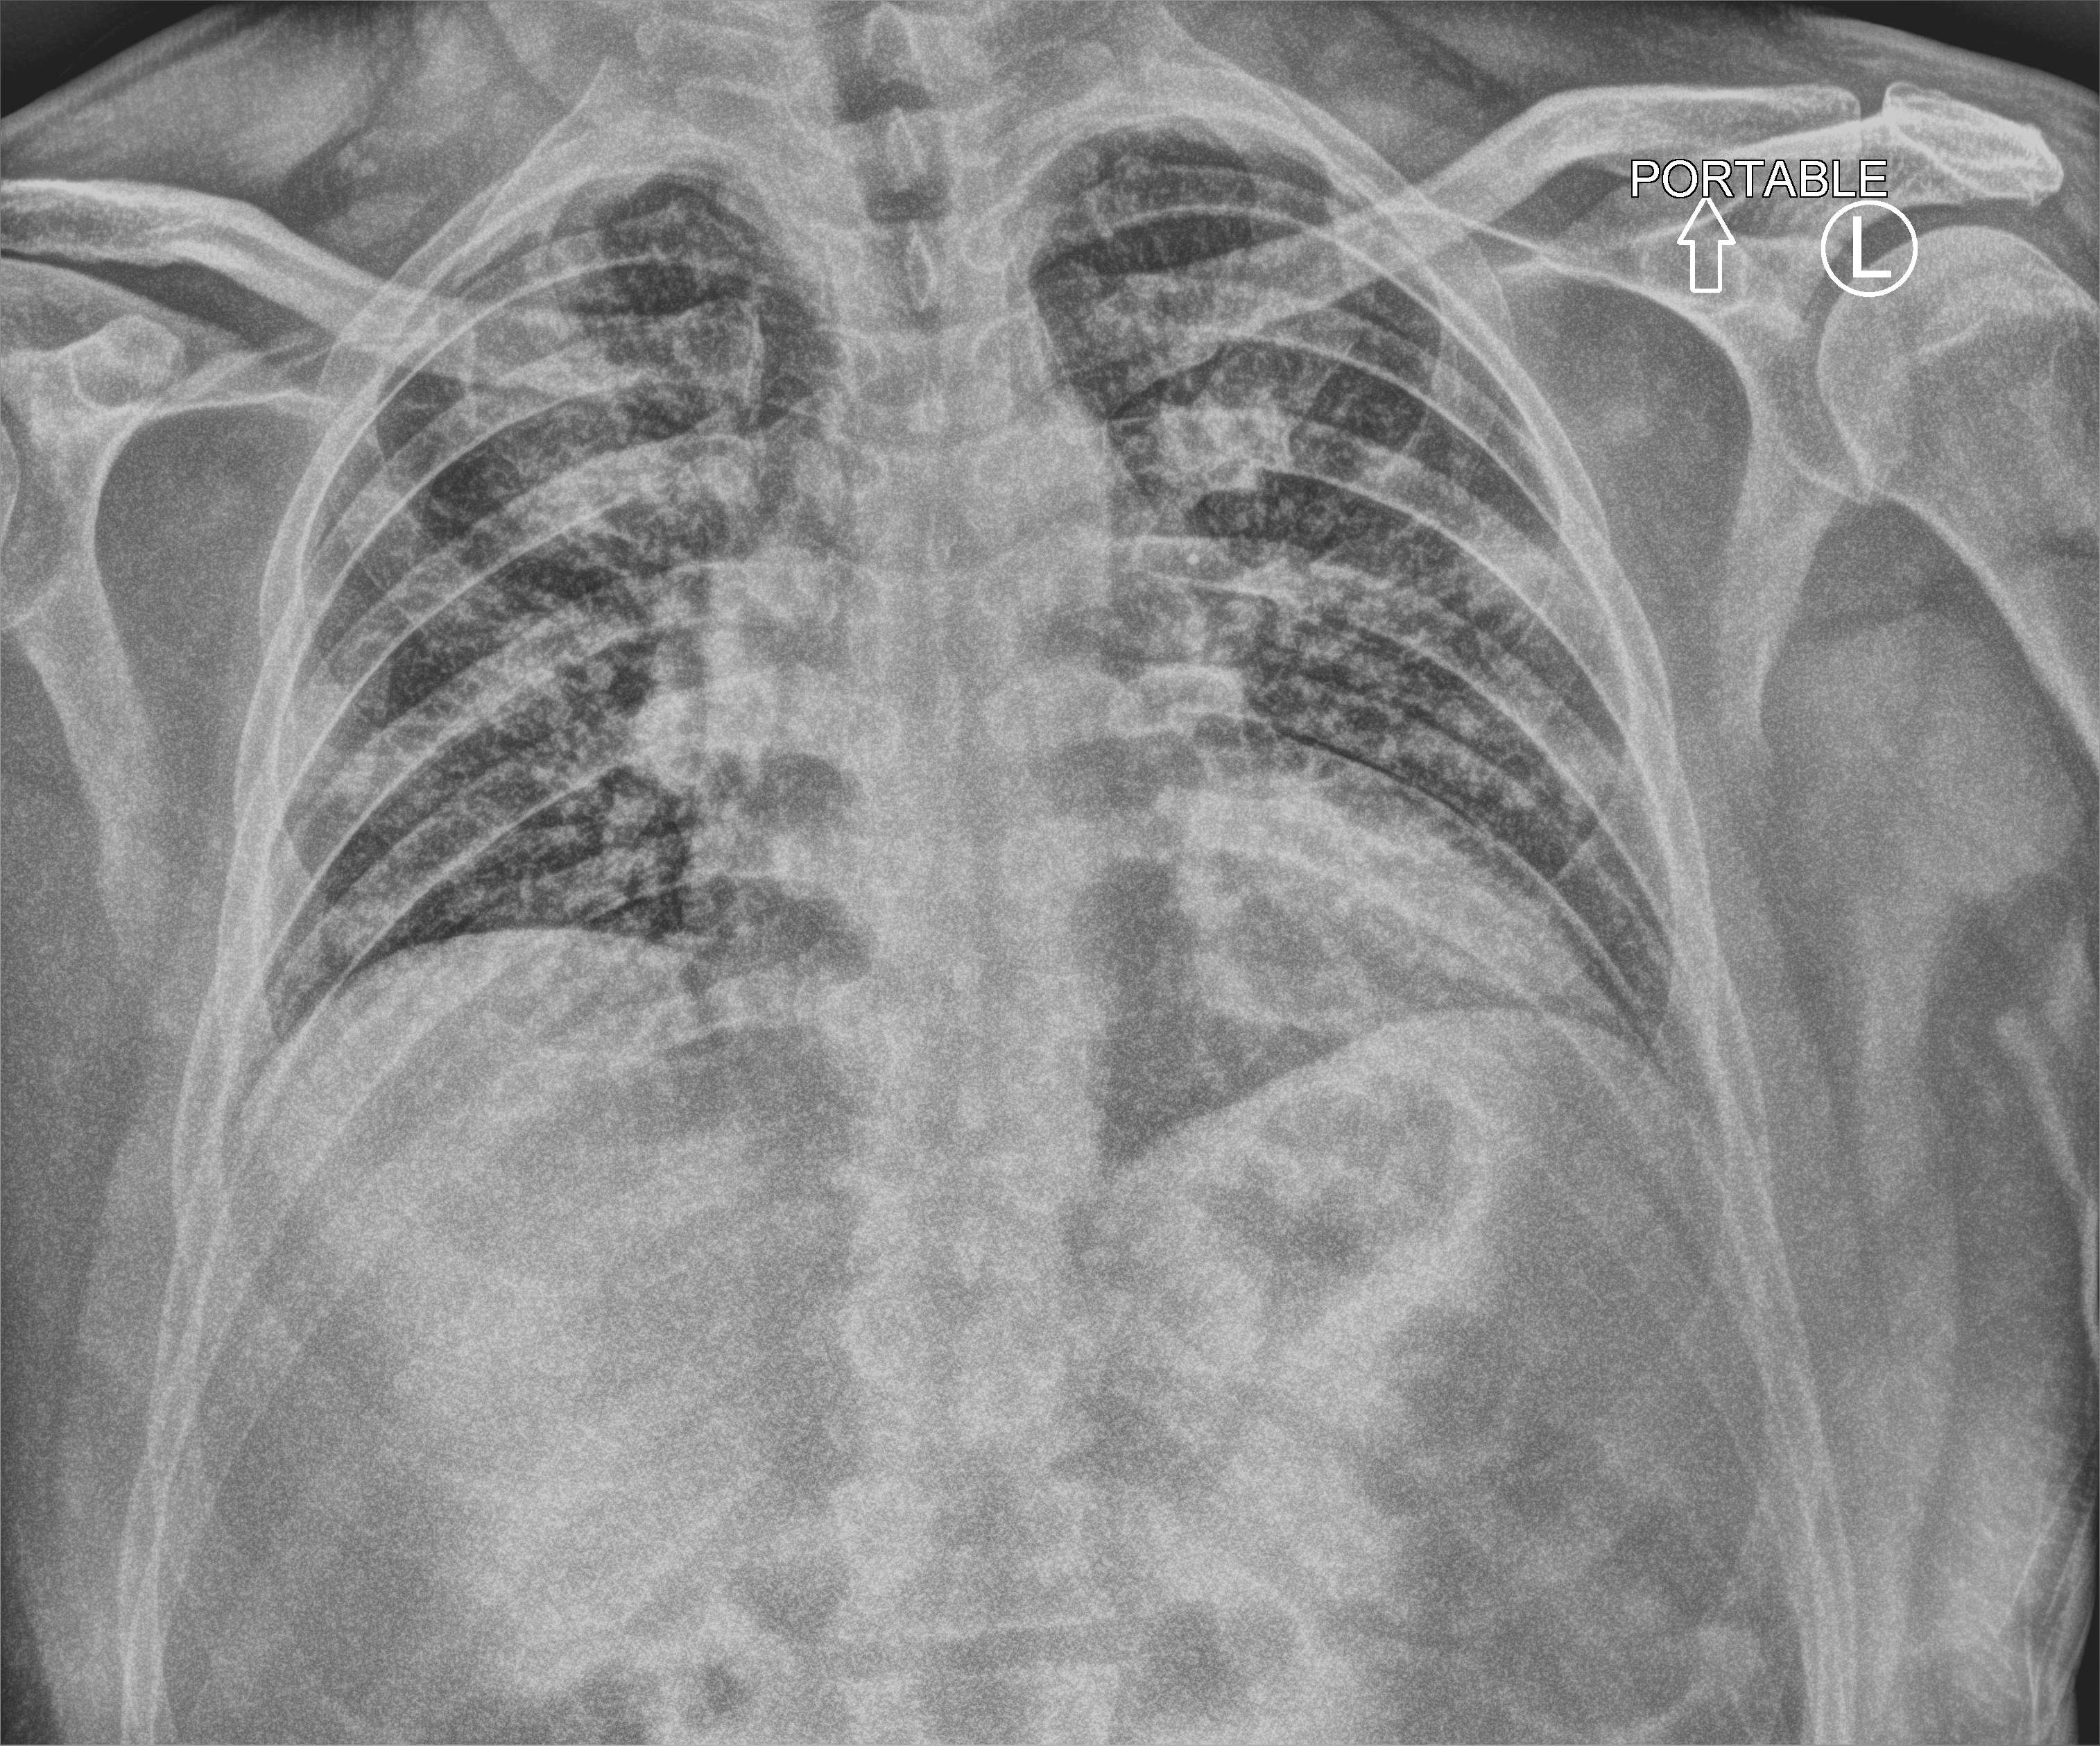
Bedside chest radiograph (computed radiography); anteroposterior (AP) projection. Male patient hospitalised with COVID-19, age 18–59 years.
Hospital-stay facts (about this admission, not read from this image; timing relative to this image not recorded): mechanically ventilated during this hospital stay: yes; admitted to intensive care during this hospital stay: no.